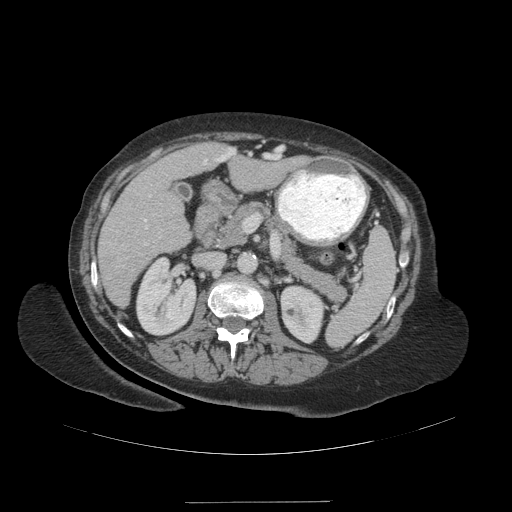
Contrast-enhanced abdominal CT (liver protocol), one axial slice; slice 52 of 99 in the series (ordered by position); 140 kVp; soft-tissue window (W 400 / L 40 HU); 2.5 mm slice thickness; 512 × 512 image matrix, field of view 440 × 440 mm. From the clinical record (not read from this slice): diagnosis: hepatocellular carcinoma (patient treated with transarterial chemoembolisation; whether this scan precedes or follows treatment is not stated here); TNM stage (as recorded): Stage-IVA; Child-Pugh class: A; tumour nodularity: multinodular.
Structures marked on this image (semi-automatic segmentation, software-assisted and operator-edited):
- liver parenchyma outside the tumour (the mass and vessels are separate outlines, so this box may not span the whole liver): bounding box <98,144,289,306> (left, top, right, bottom; pixels)
- liver vessels: <102,148,236,246>